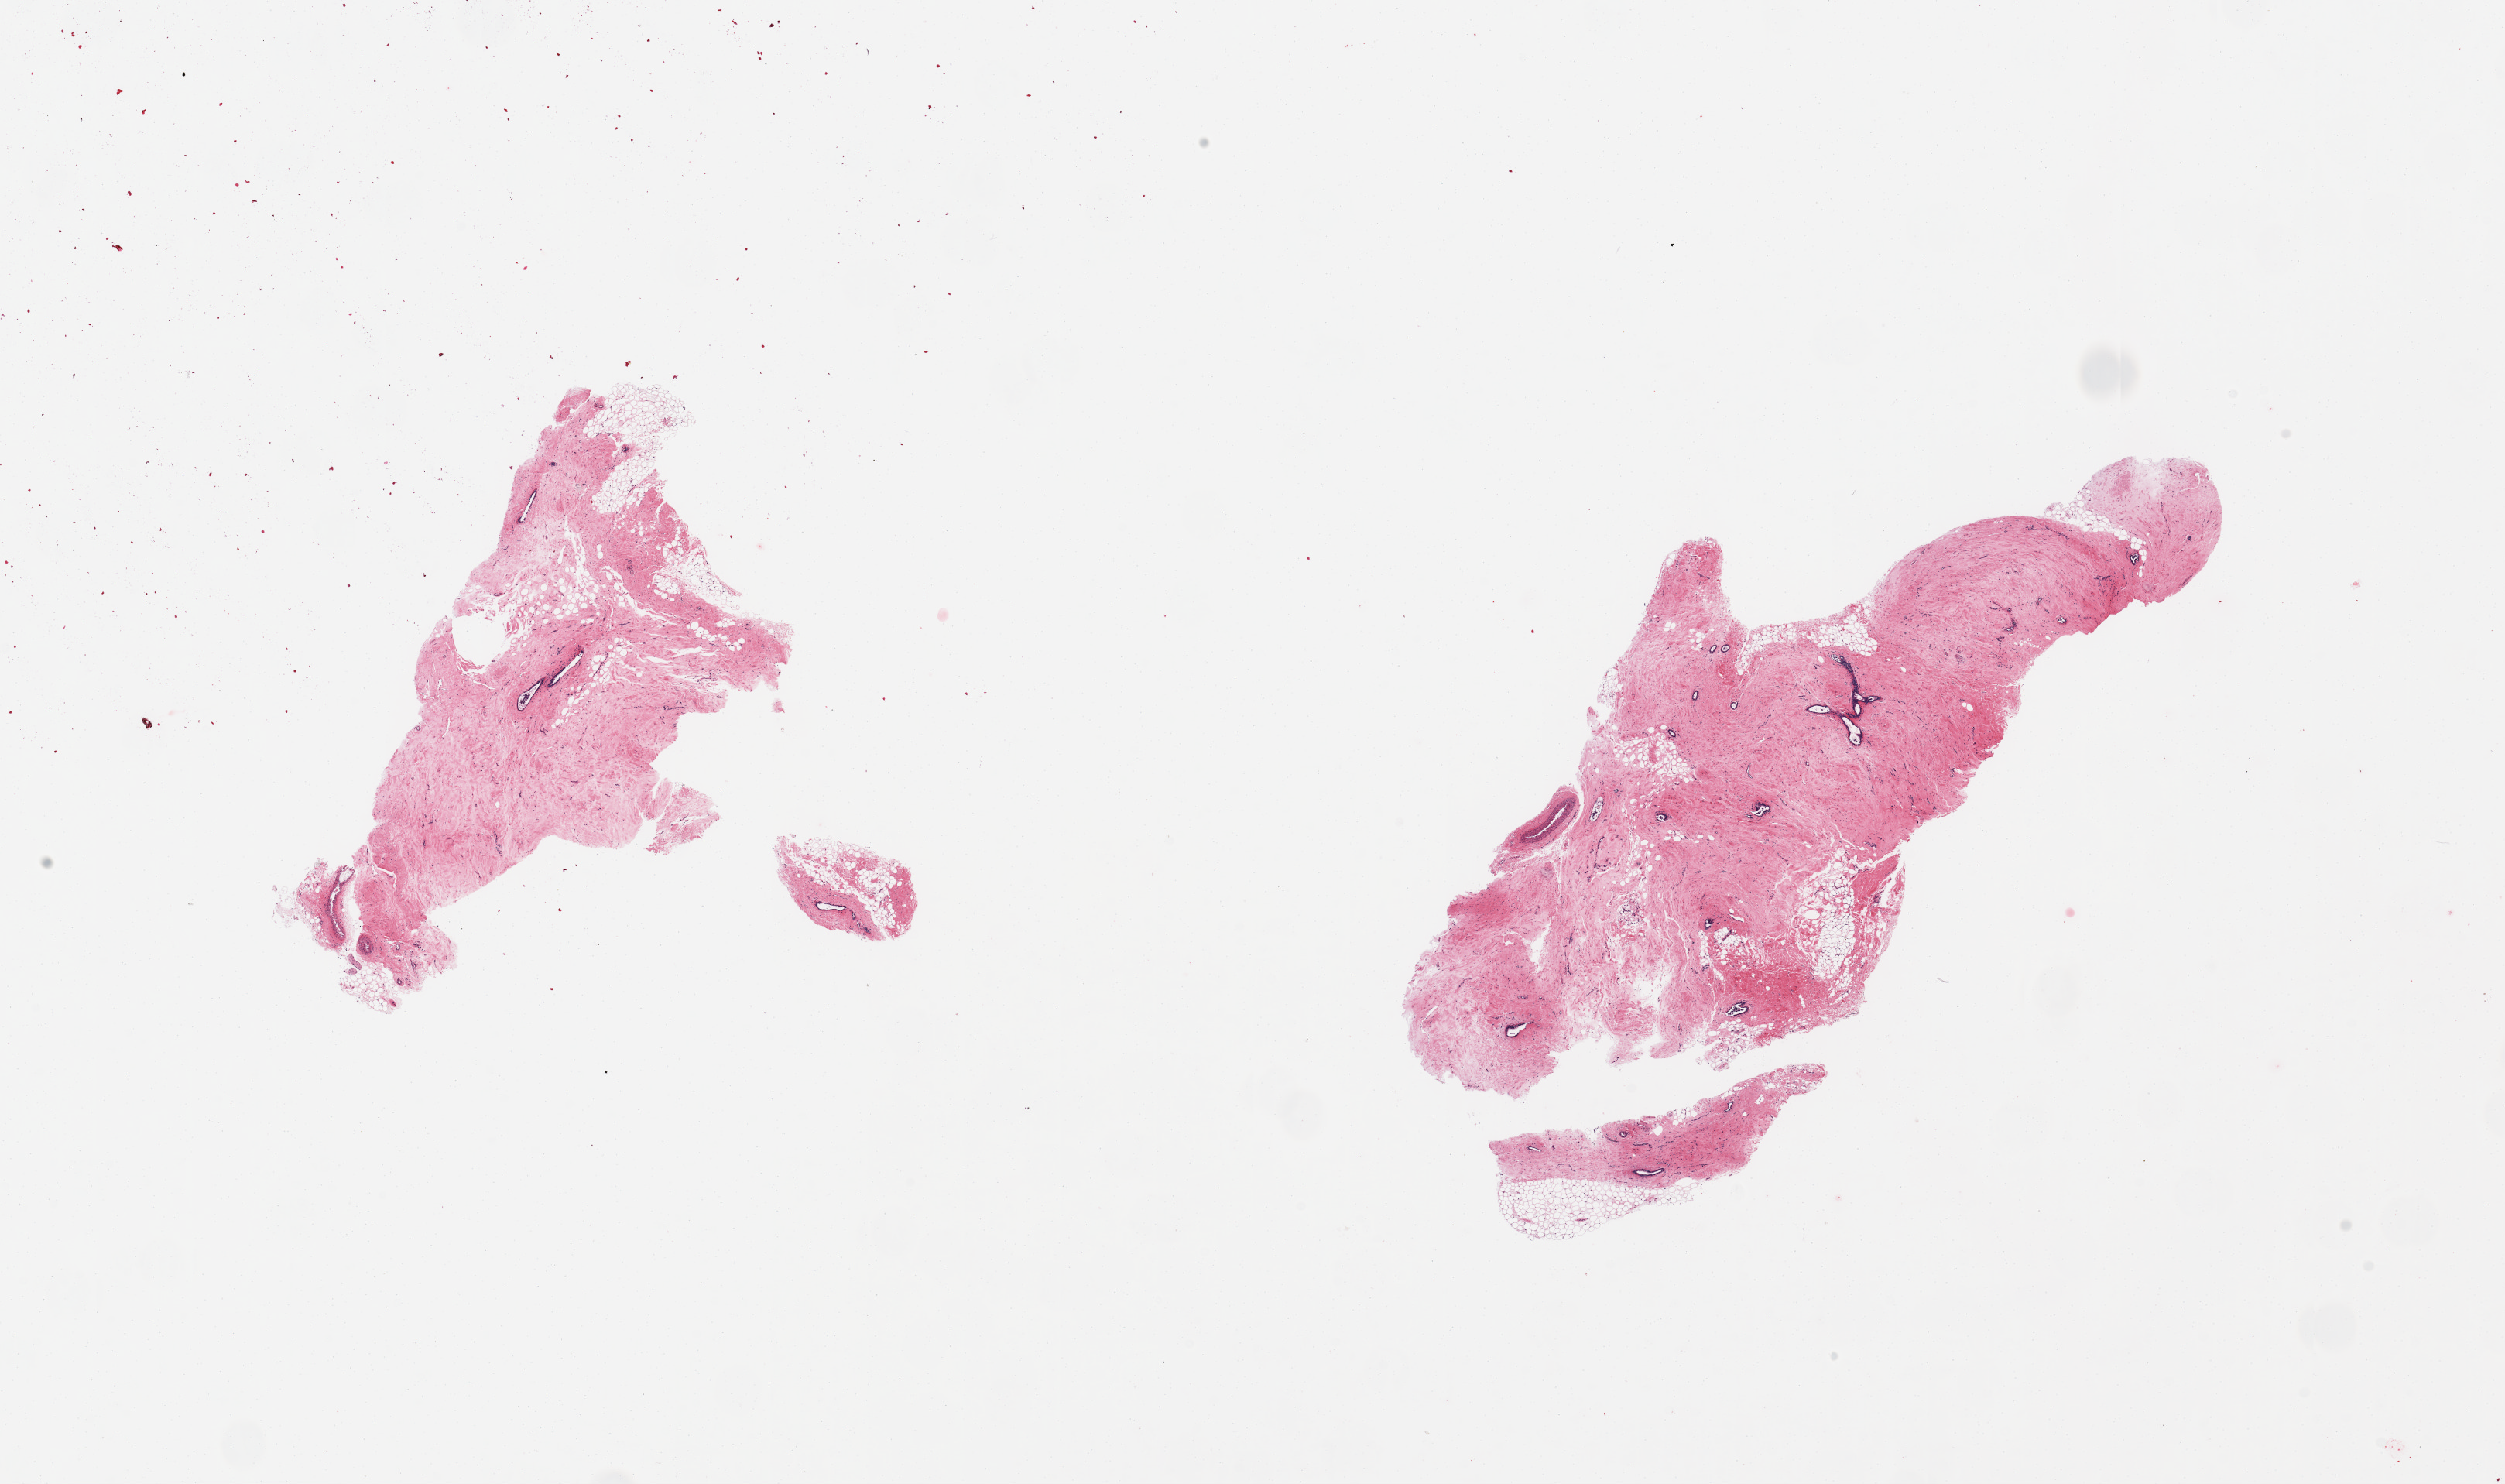
Hematoxylin and eosin (H&E) whole-slide image, brightfield, a low-resolution overview of the entire scanned area, about 25.6 x 15.2 mm (acquisition: 20x scan), PAXgene-fixed, paraffin-embedded tissue, target tissue: breast, donor tissue sample. Donor sex: male.
Reviewer comment on this tissue sample: 2 pieces; predominantly fibrocollagenous stroma with scattered ducts, minor component of fat.